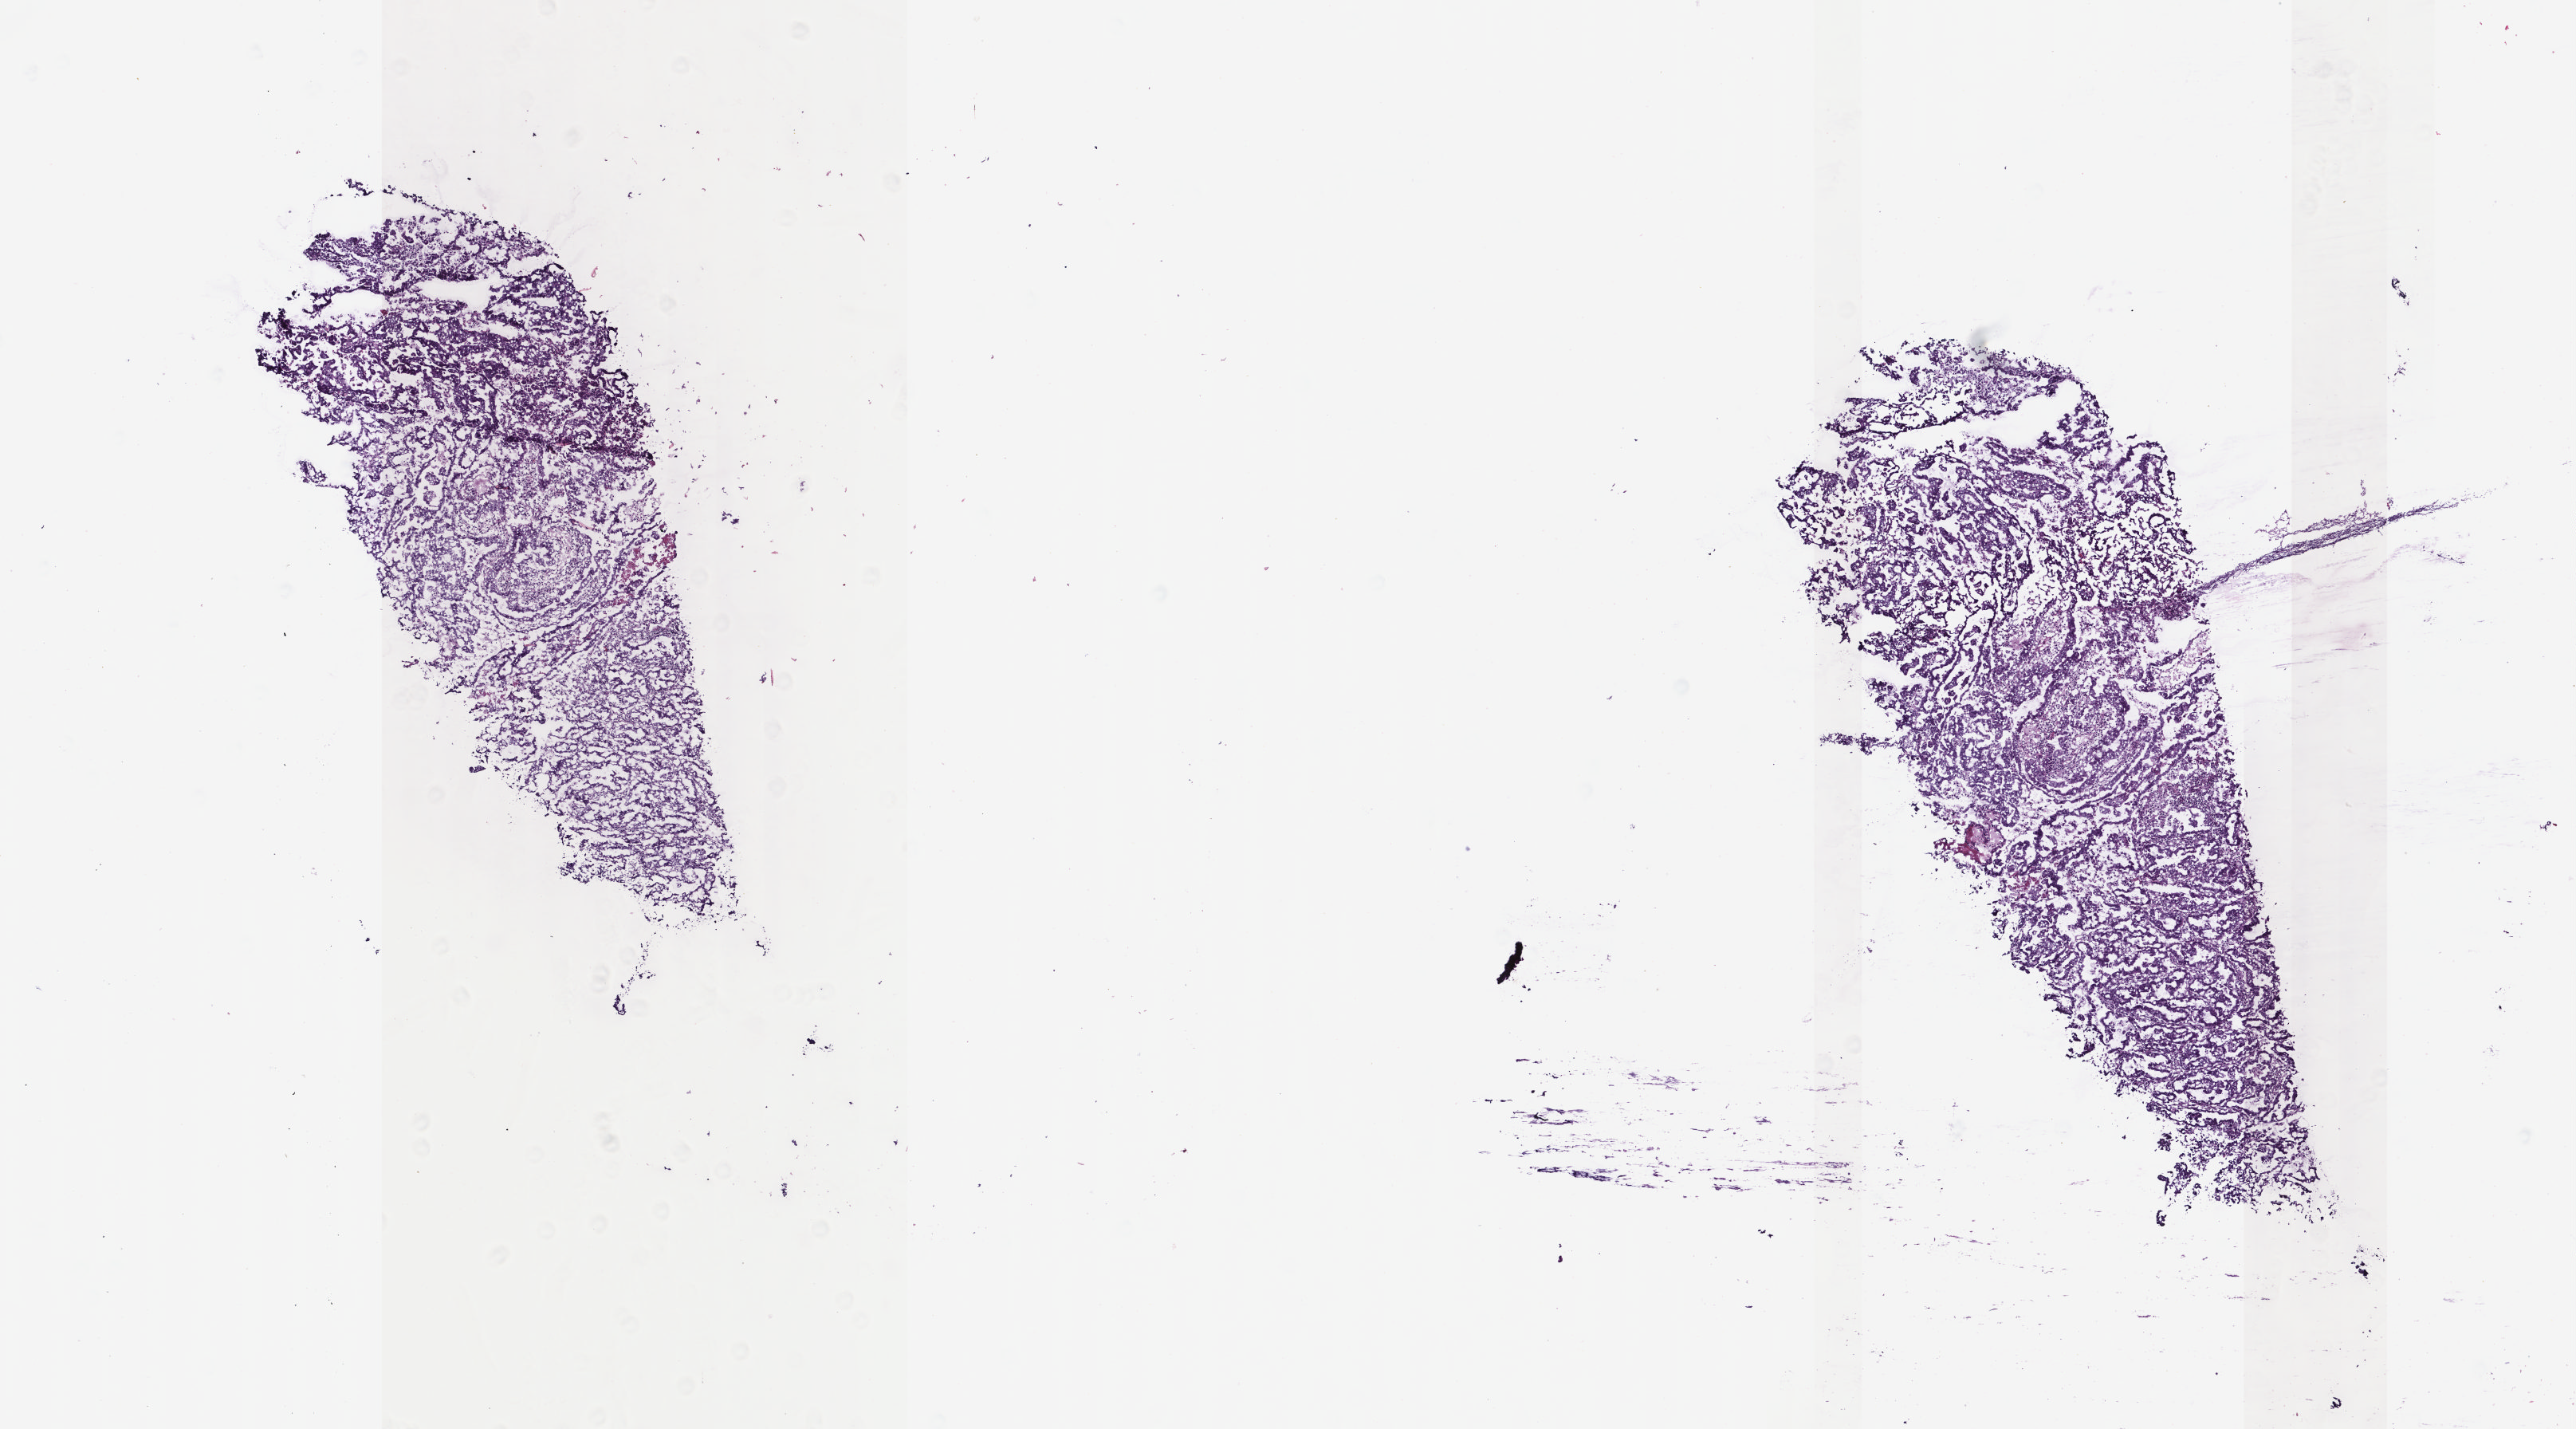
Digitized H&E tissue section (whole slide), shown as a low-resolution overview of the whole scanned area (about 12.8 x 7.1 mm), frozen section, uterus, primary tumour sample. Patient: female, age at initial diagnosis 79 years. Histologic grade: G3 (poorly differentiated). Pathologist review of this section (percent, as recorded): tumour cells 55%, tumour nuclei 85%, normal cells 0%, stromal cells 15%, necrosis 30%. Infiltration values recorded for this section: lymphocyte infiltration 7%, monocyte infiltration 0%, neutrophil infiltration 1%.
* diagnosis: Serous cystadenocarcinoma, NOS (endometrium)
* FIGO stage: IIIC